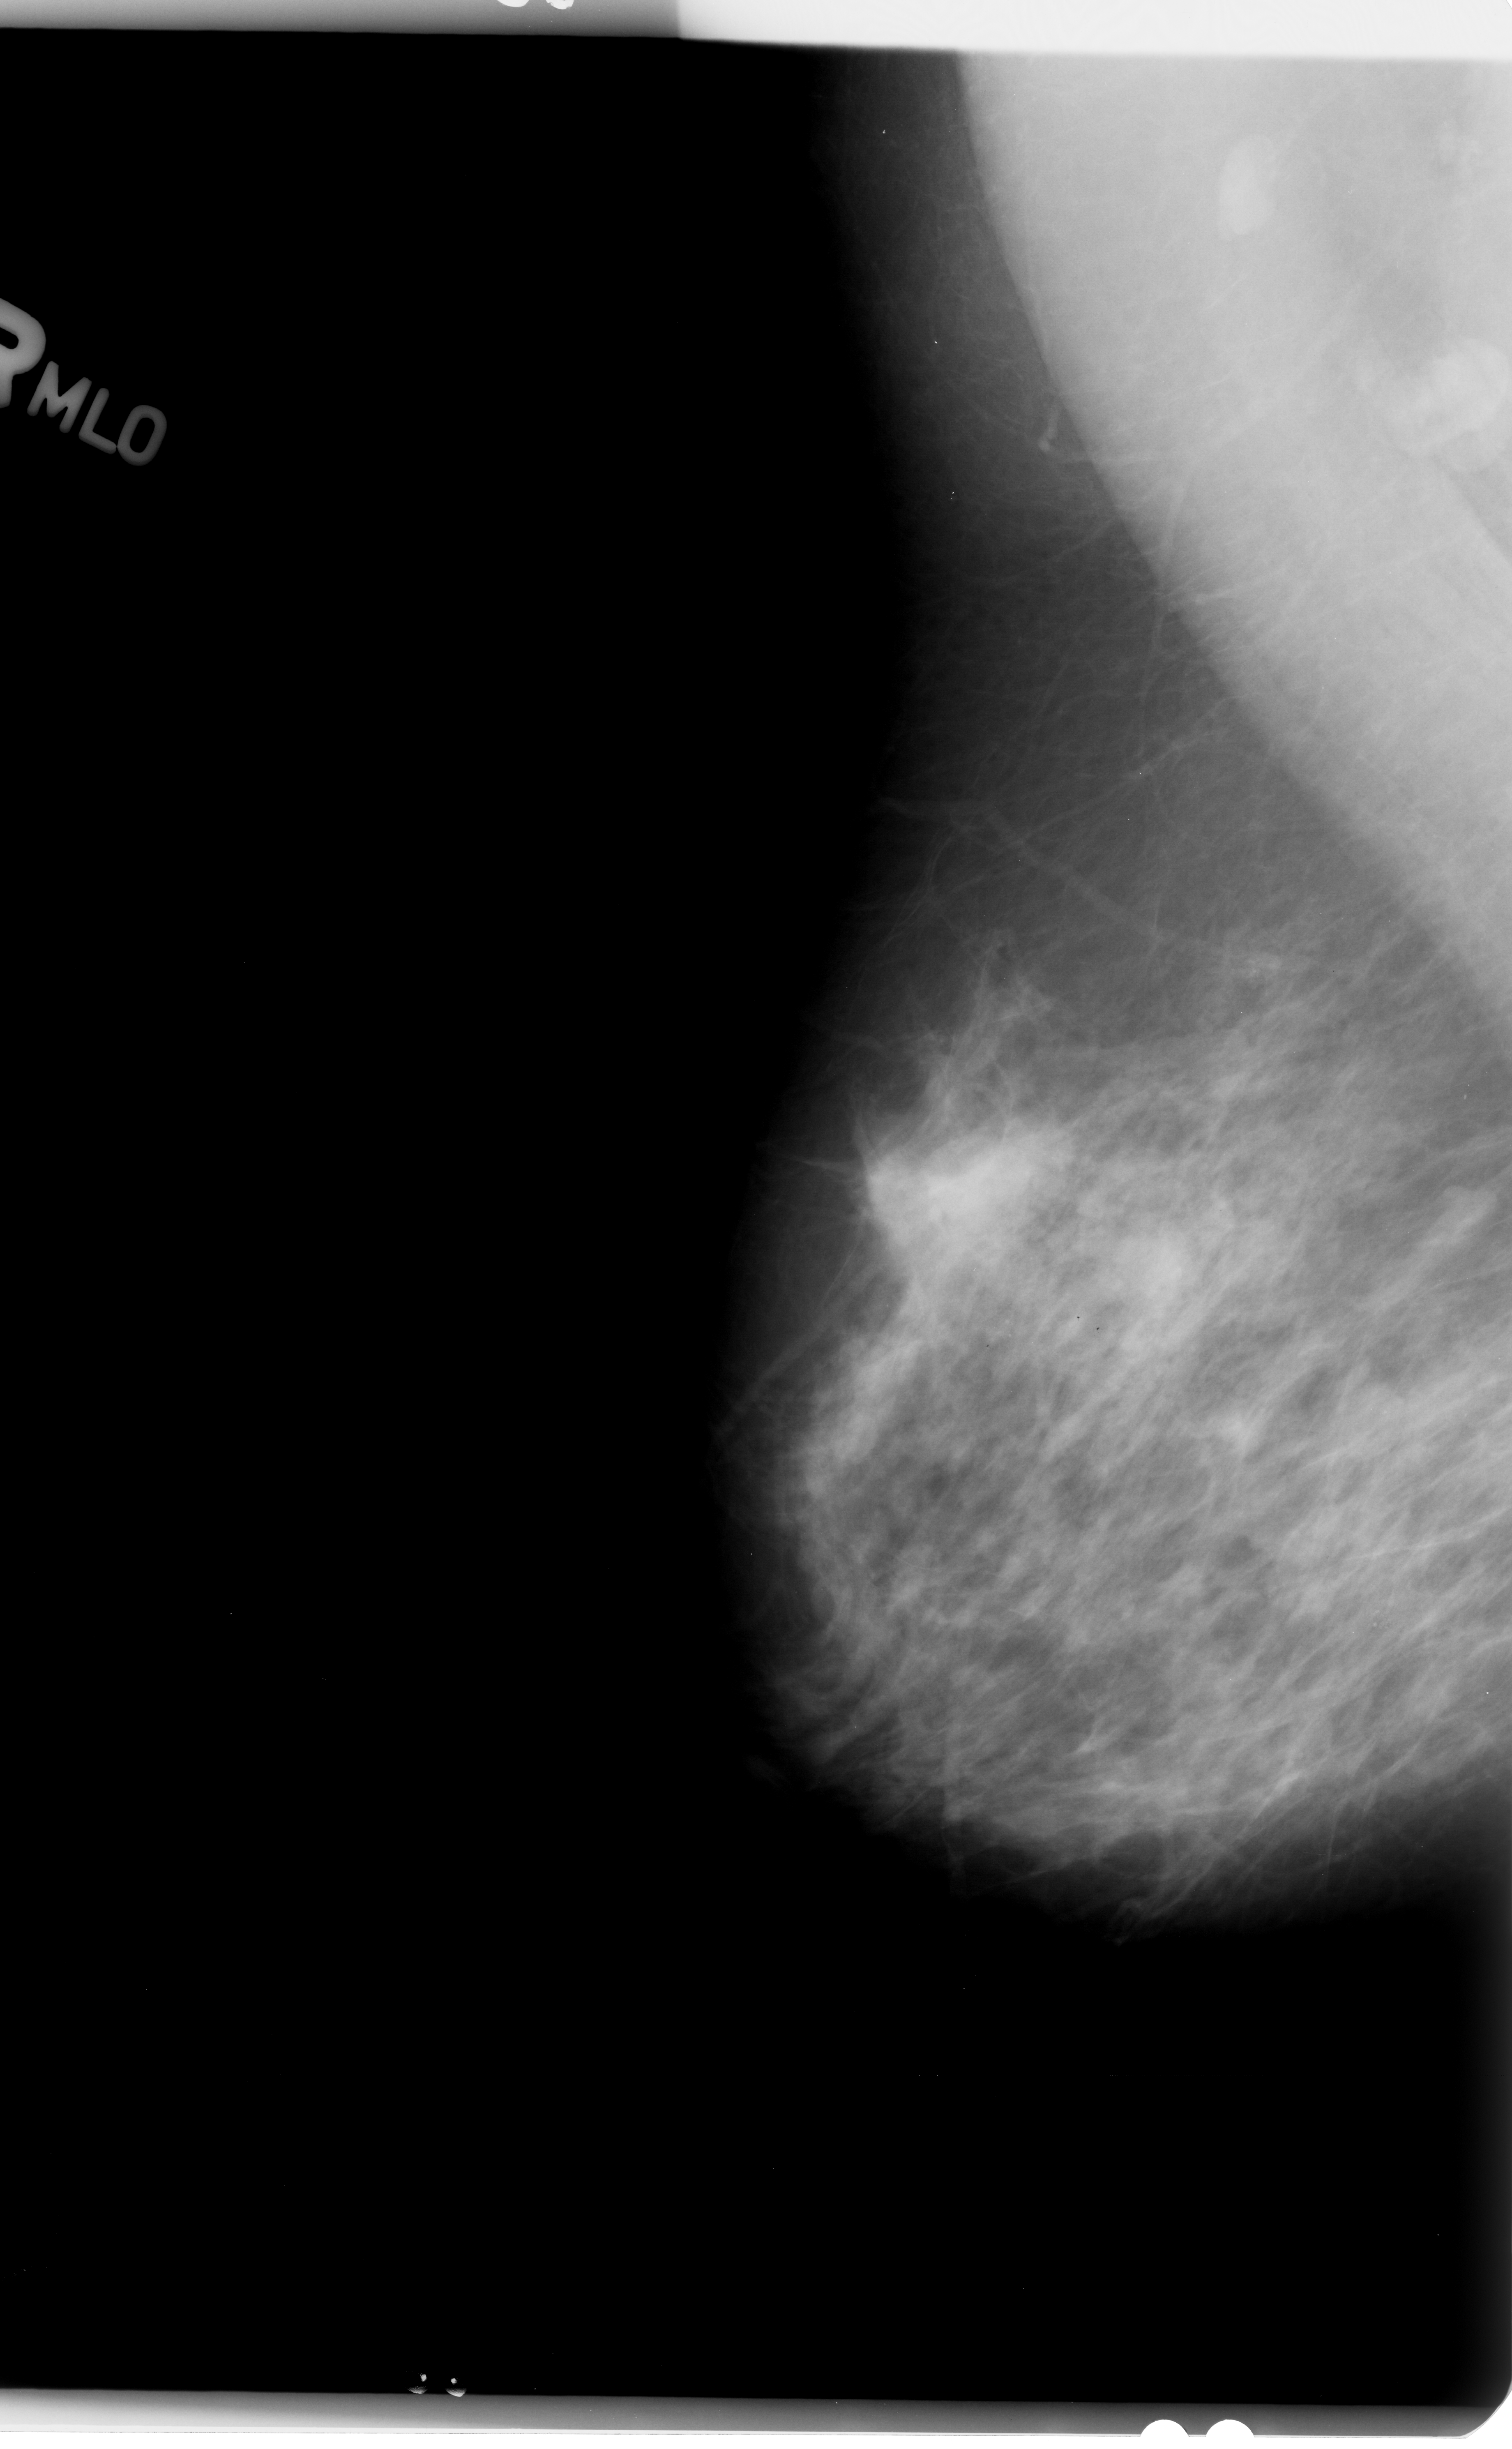
Mammogram (digitized film). Right breast. MLO view. BI-RADS breast density category 3 (scale 1–4). 1512 × 2449 image matrix.
Expert-marked regions of interest on this film, with their recorded descriptors:
- Finding 1 of 2: calcifications, morphology amorphous / pleomorphic, distribution clustered; BI-RADS assessment category 4; subtlety rating 2 on a 1 (subtle) to 5 (obvious) scale; pathology (as recorded): benign: bounding box (x1, y1, x2, y2) in pixels: (976, 1282, 1046, 1368)
- Finding 2 of 2: calcifications, morphology amorphous / pleomorphic, distribution clustered; BI-RADS assessment category 4; pathology result (as recorded, not read from the image): benign: (1367, 1521, 1457, 1618)